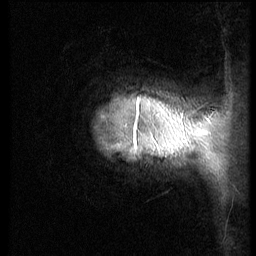
Breast MRI (dynamic contrast-enhanced), one sagittal slice. Position 7 of 70 along the scan axis. 3 images stored at this slice position (order not interpretable as contrast timing). 1.5 T. TE 4.2 ms, TR 9 ms. 2.5 mm slice thickness. 256 × 256 image matrix, field of view 180 × 180 mm. Female patient, age 28 years. From the clinical record (not read from this slice): setting: breast cancer imaged before/during neoadjuvant chemotherapy.
Structures marked on this image (semi-automatically segmented with operator editing):
- analysis volume of interest (the breast-tissue region the enhancement analysis was run in; not a lesion): bounding box <80,60,186,211> (left, top, right, bottom; pixels)
- tumour enhancement mask (voxels above the 140 % enhancement threshold inside the analysis volume of interest): <135,106,139,135>